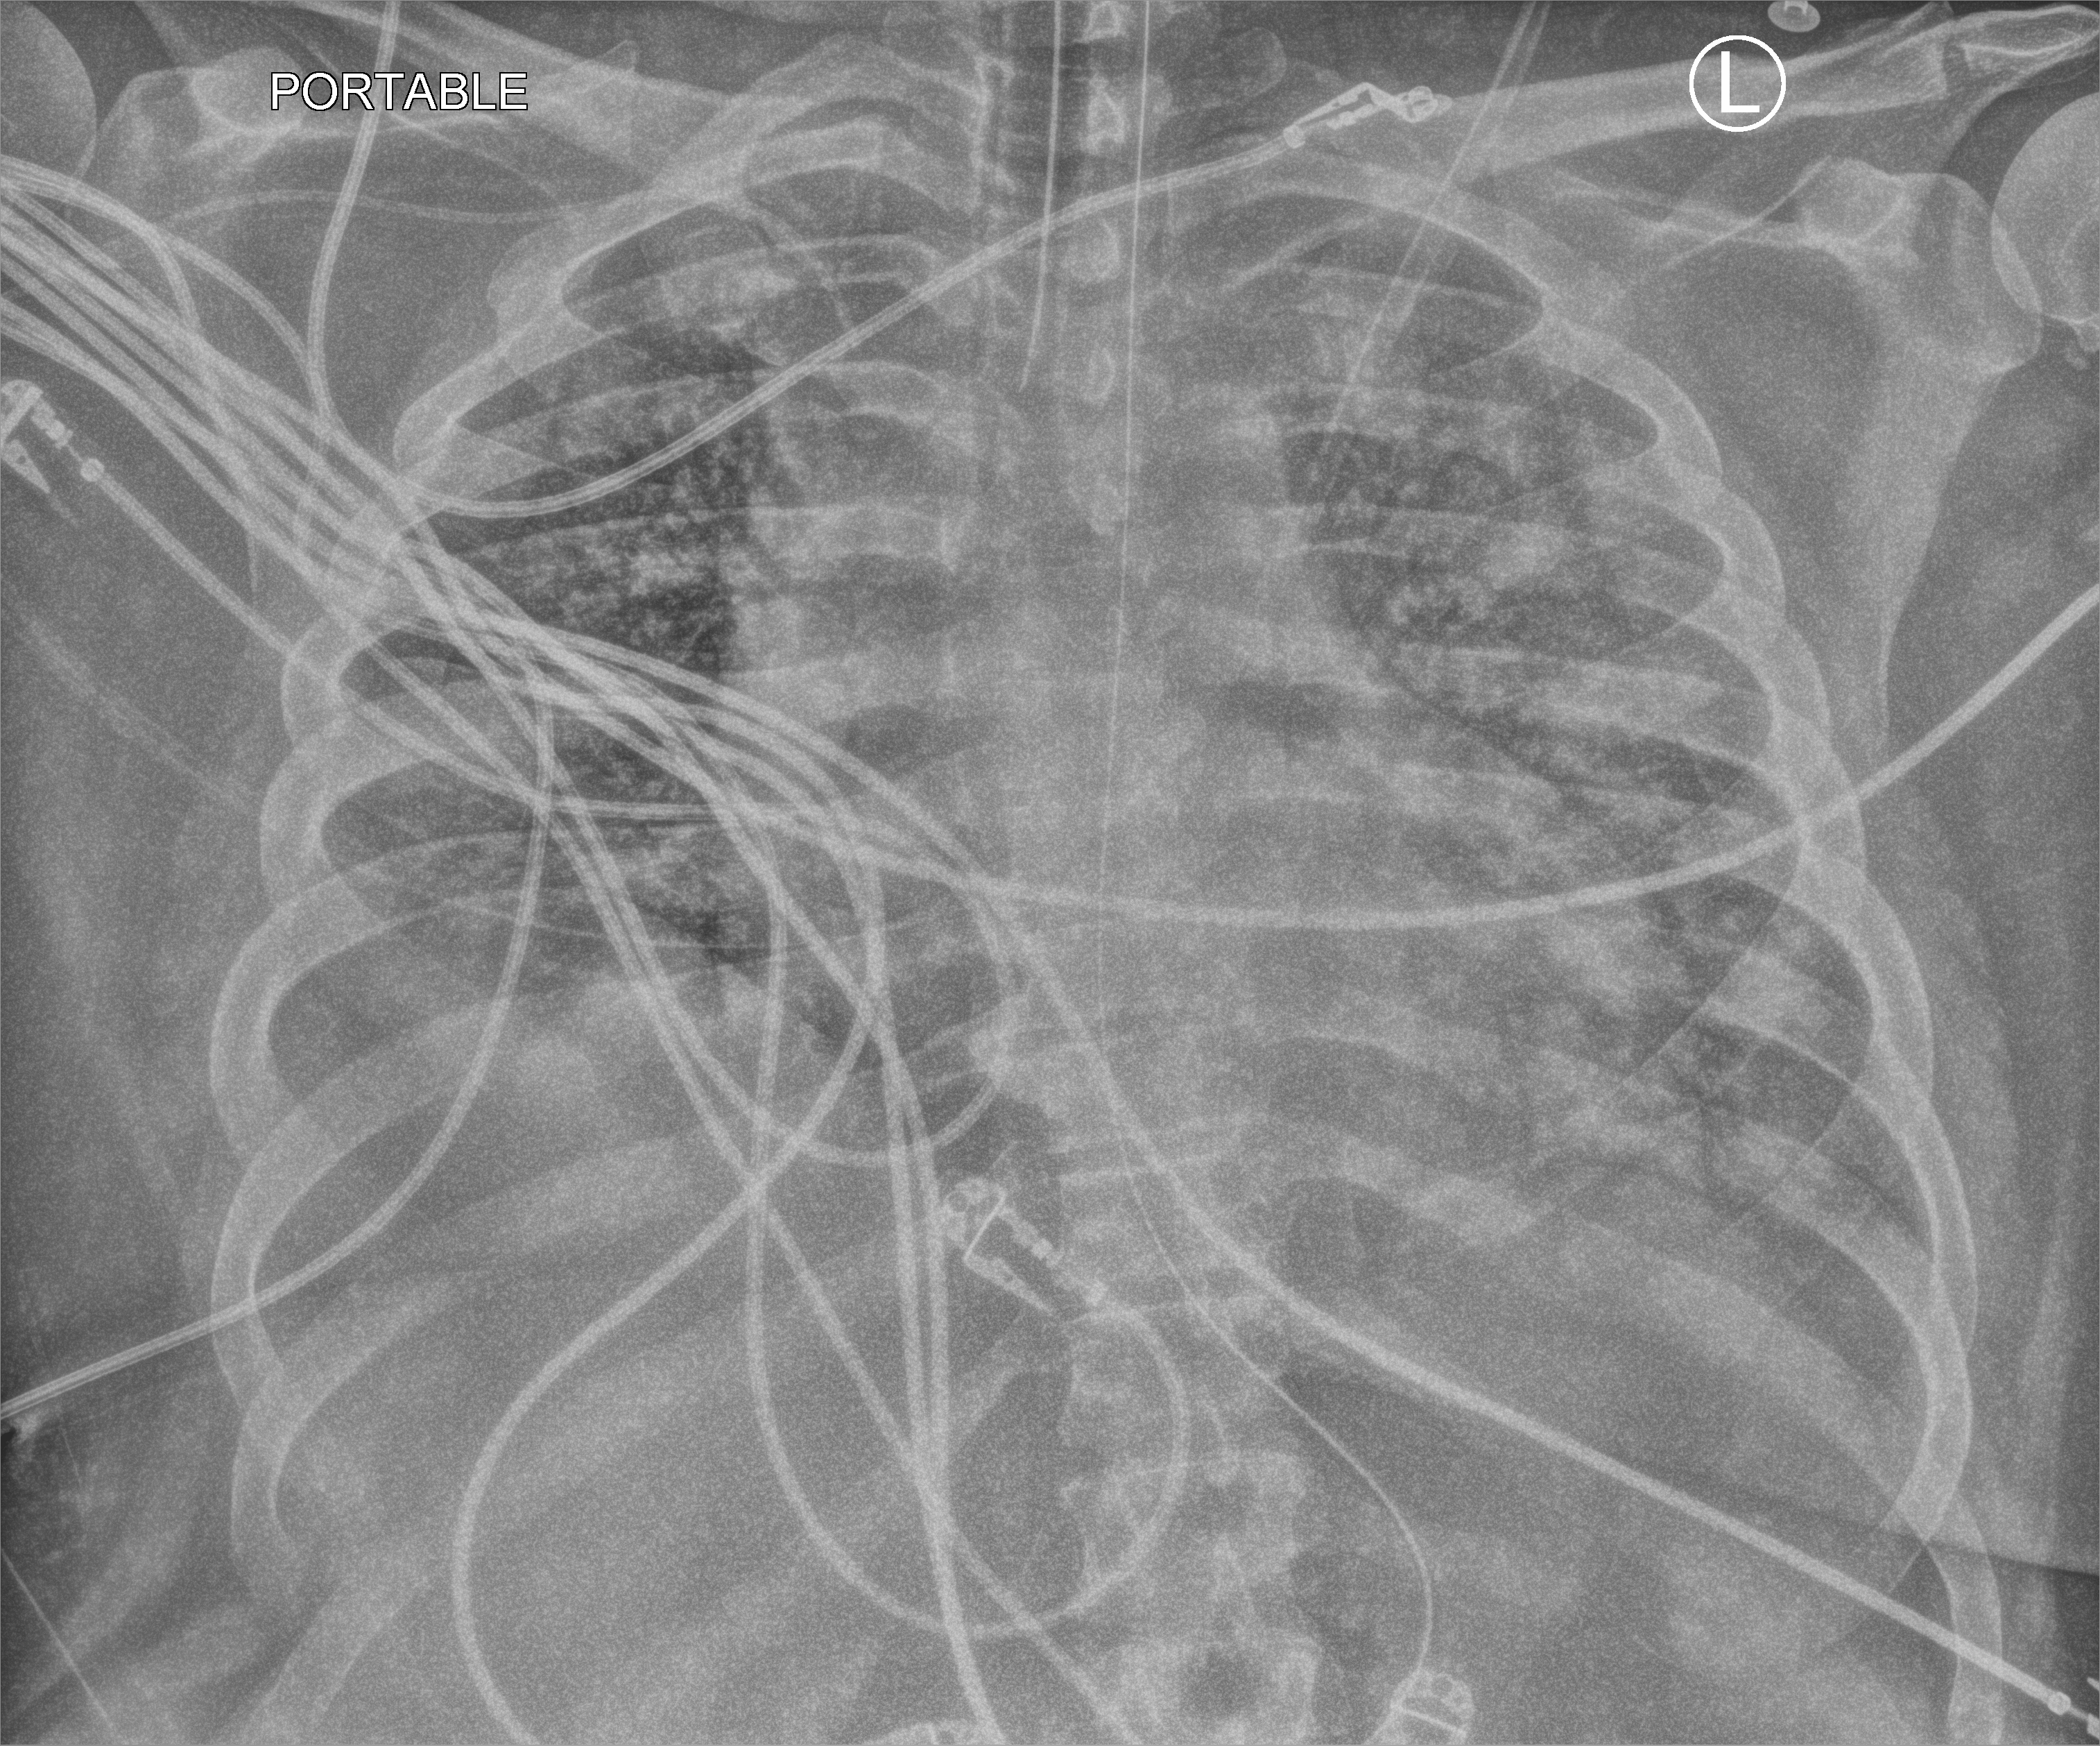
Bedside chest radiograph (computed radiography), anteroposterior (AP) projection. Patient hospitalised with COVID-19, aged 18–59 years.
Admission-level facts for this patient (not findings on this image; timing relative to this image not recorded): mechanically ventilated during this hospital stay: yes.